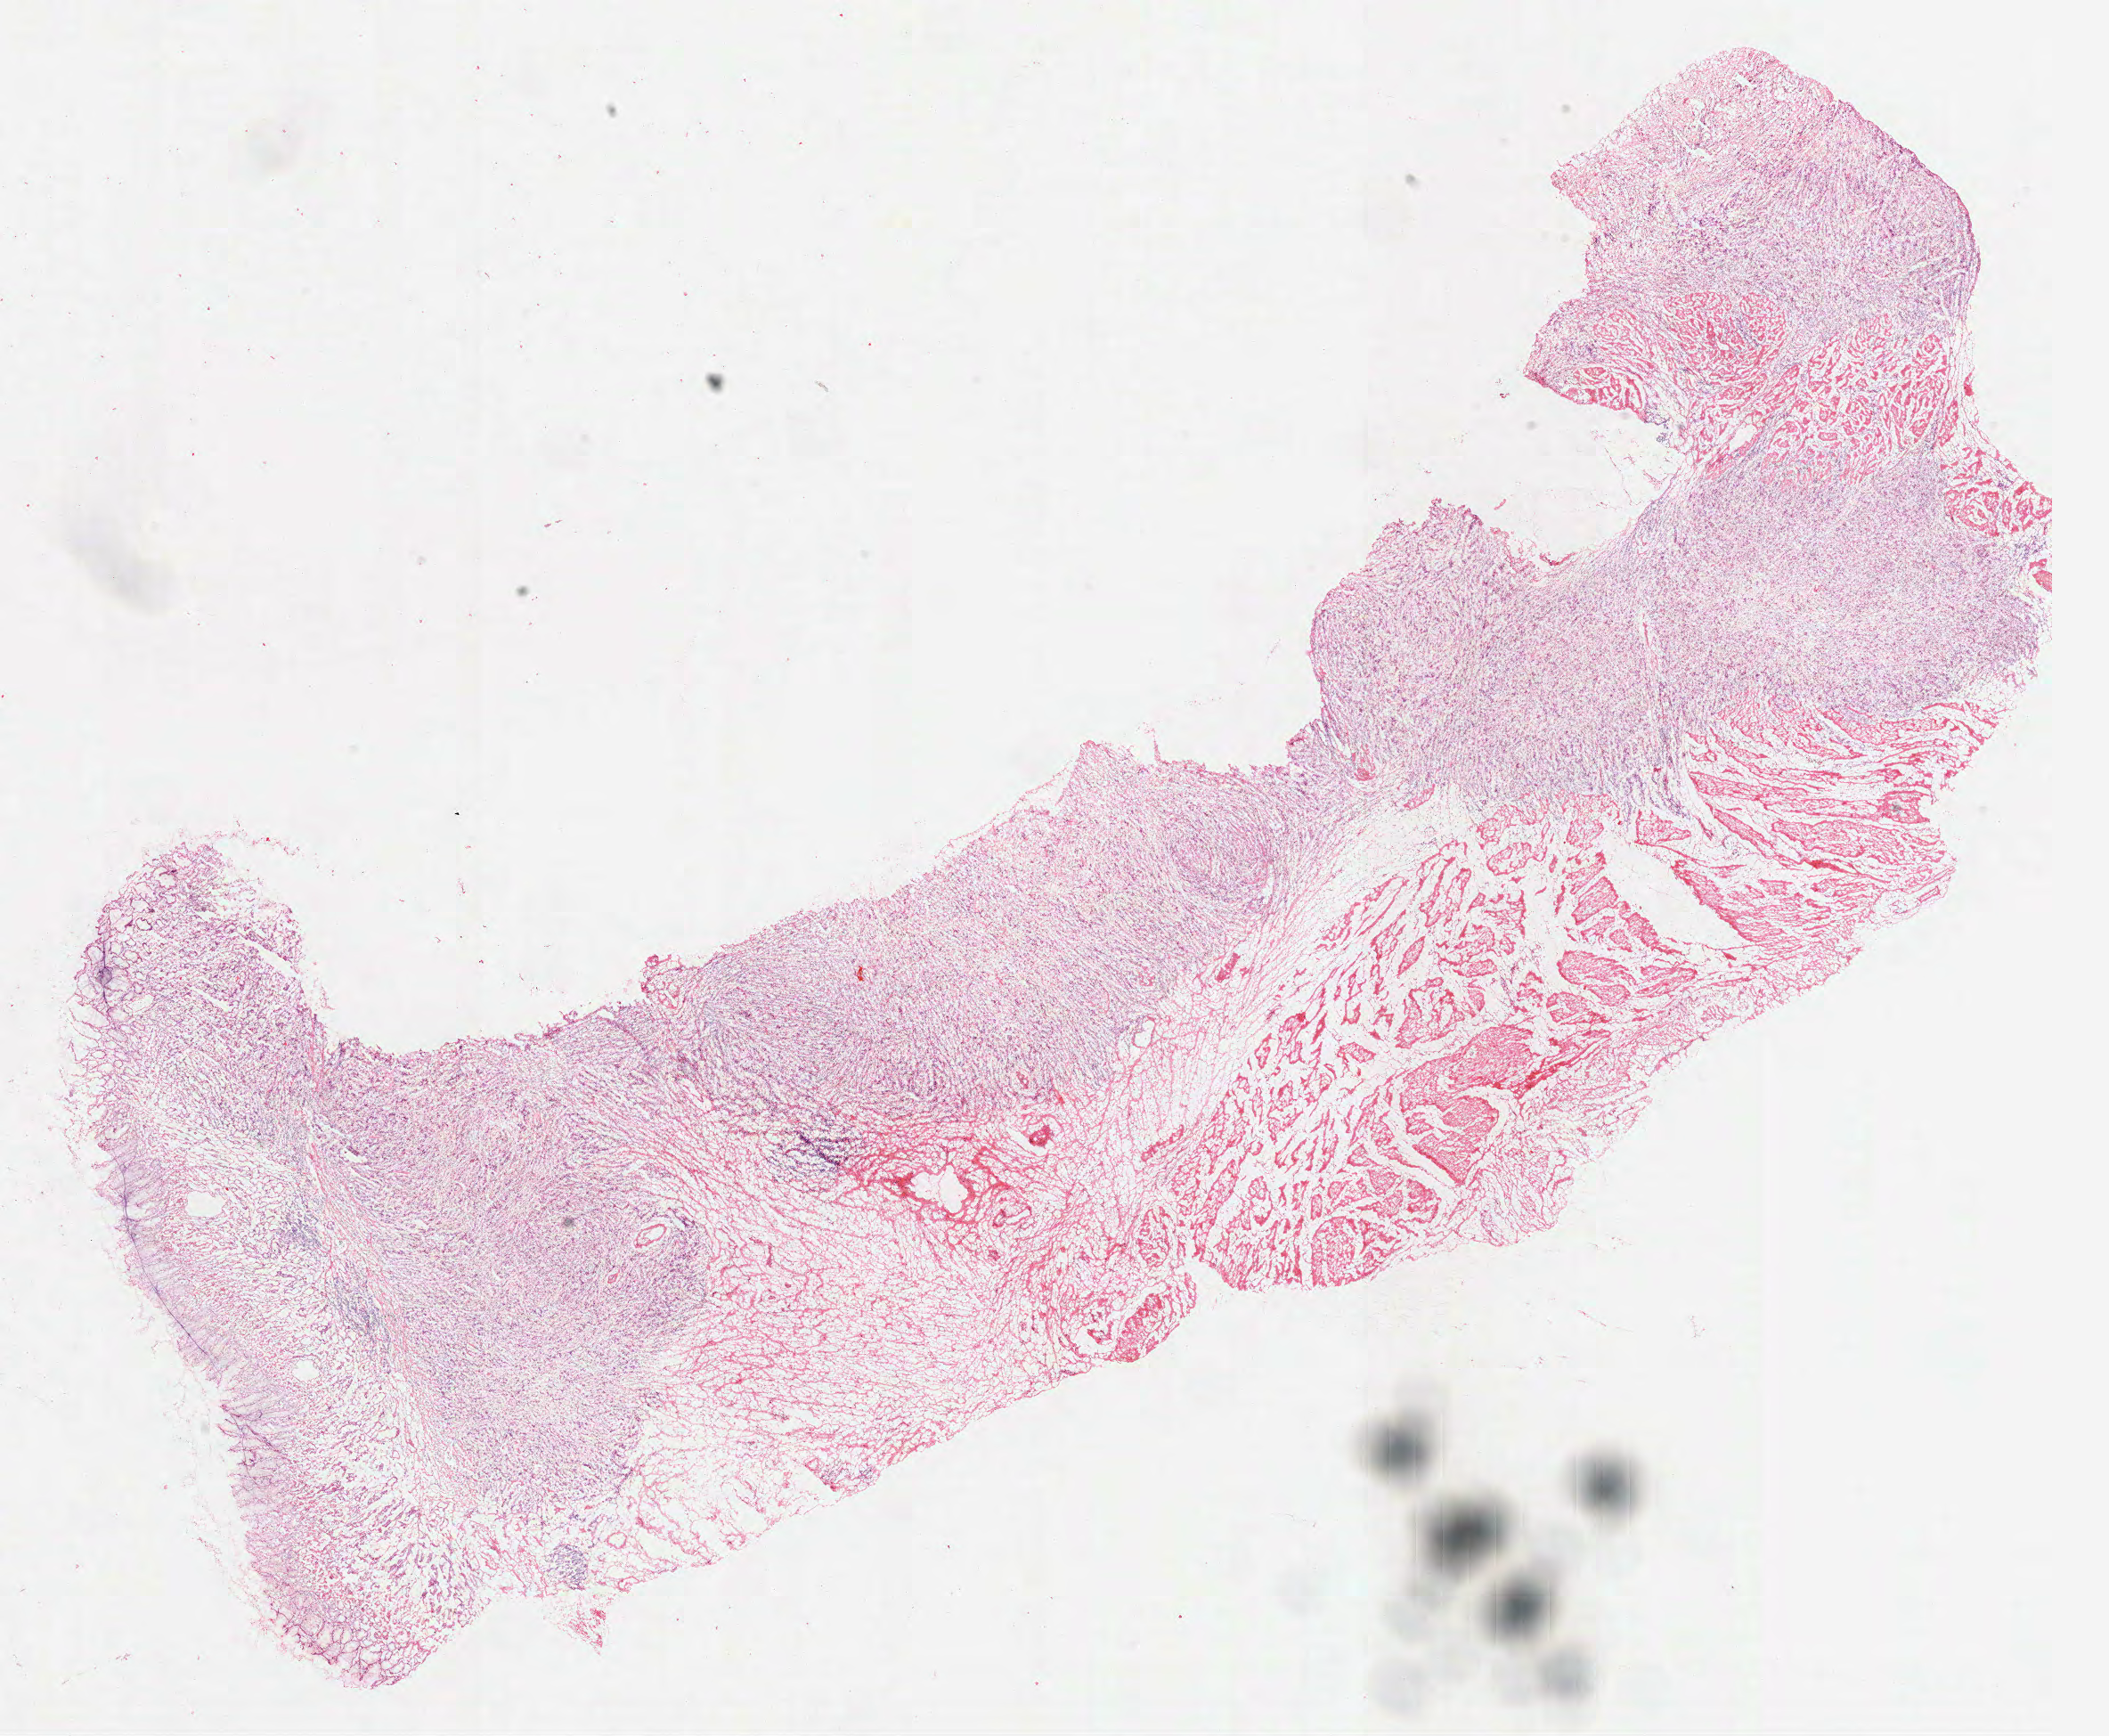
Hematoxylin and eosin (H&E) stained whole-slide image, whole scanned area (about 19.1 x 15.7 mm, acquisition: 40x scan) shown as a low-resolution overview. Frozen section from the top of the tissue portion. Sample: primary tumour, stomach. Female, age 55 years at initial diagnosis. Histologic grade: G3 (poorly differentiated). Composition of this section per pathologist review: tumour cells 62%, tumour nuclei 70%, normal cells 8%, stromal cells 30%, necrosis 0%.
Lymph nodes positive (case pathology): 0 of 6 examined. AJCC pathologic stage: IIB (7th edition). Pathologic diagnosis: Adenocarcinoma, NOS.